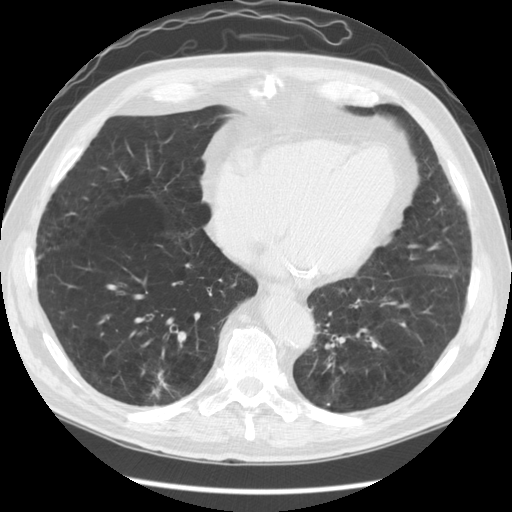
Low-dose screening chest CT, one axial slice; slice 48 of 141 in the series (ordered by position); 120 kVp; lung window (W 1500 / L -600 HU); 512 × 512 image matrix, field of view 370 × 370 mm.
Structures marked on this image (outlined manually by an expert reader):
- lesion 1 (tumor, lower lobe of right lung): bounding box <152,383,167,398> (left, top, right, bottom; pixels)